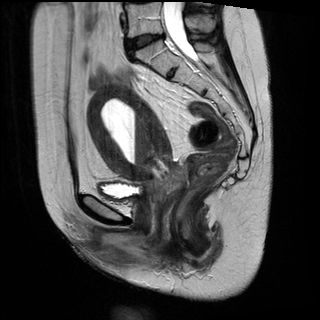
Pelvic MRI for cervical cancer, one sagittal slice. Slice 13 of 28 in the series (ordered by position). T2-weighted. 1.5 T. TE 89 ms, TR 2740 ms. 4 mm slice thickness. 320 × 320 image matrix, field of view 260 × 260 mm. Patient: female, 49 years.
Outlined on this slice (manually delineated by an expert):
- uterus and cervix: bounding box [x1, y1, x2, y2] px = [85, 83, 188, 204]